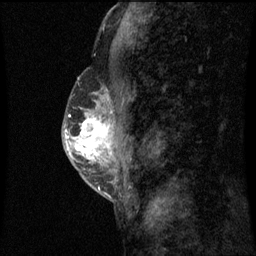
Breast MRI (dynamic contrast-enhanced), one sagittal slice. Position 28 of 60 along the scan axis. Dynamic contrast-enhanced series, image 2 of 3 at this slice position (ordered by acquisition). 1.5 T. TE 4.2 ms, TR 8.9 ms. 2 mm slice thickness. 256 × 256 image matrix, field of view 200 × 200 mm. Patient: female, 50 years. From the clinical record (not read from this slice): setting: breast cancer imaged before/during neoadjuvant chemotherapy; receptor status: triple-negative.
Annotated regions visible in this slice (semi-automatically segmented with operator editing):
- analysis volume of interest (the breast-tissue region the enhancement analysis was run in; not a lesion): box from (x=68, y=80) to (x=113, y=169) px
- tumour enhancement mask (voxels above the 70 % enhancement threshold inside the analysis volume of interest): (x=68, y=116)–(x=110, y=159)